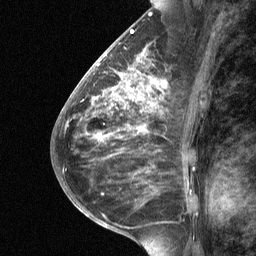
Breast MRI (dynamic contrast-enhanced), one sagittal slice; dynamic contrast-enhanced study with each time point stored as its own series, time point 2 of 3 at this slice position (early post-contrast, ordered by acquisition time); 1.5 T; TE 4.8 ms, TR 27 ms; 2 mm slice thickness; 256 × 256 image matrix. Female patient, age 59 years. From the clinical record (not read from this slice): setting: breast cancer imaged before/during neoadjuvant chemotherapy; receptor status: triple-negative.
Structures marked on this image (semi-automatic segmentation, software-assisted and operator-edited):
- analysis volume of interest (the breast-tissue region the enhancement analysis was run in; not a lesion): bounding box (x1, y1, x2, y2) in pixels: (113, 66, 167, 120)
- tumour enhancement mask (voxels above the 90 % enhancement threshold inside the analysis volume of interest): (116, 74, 157, 105)